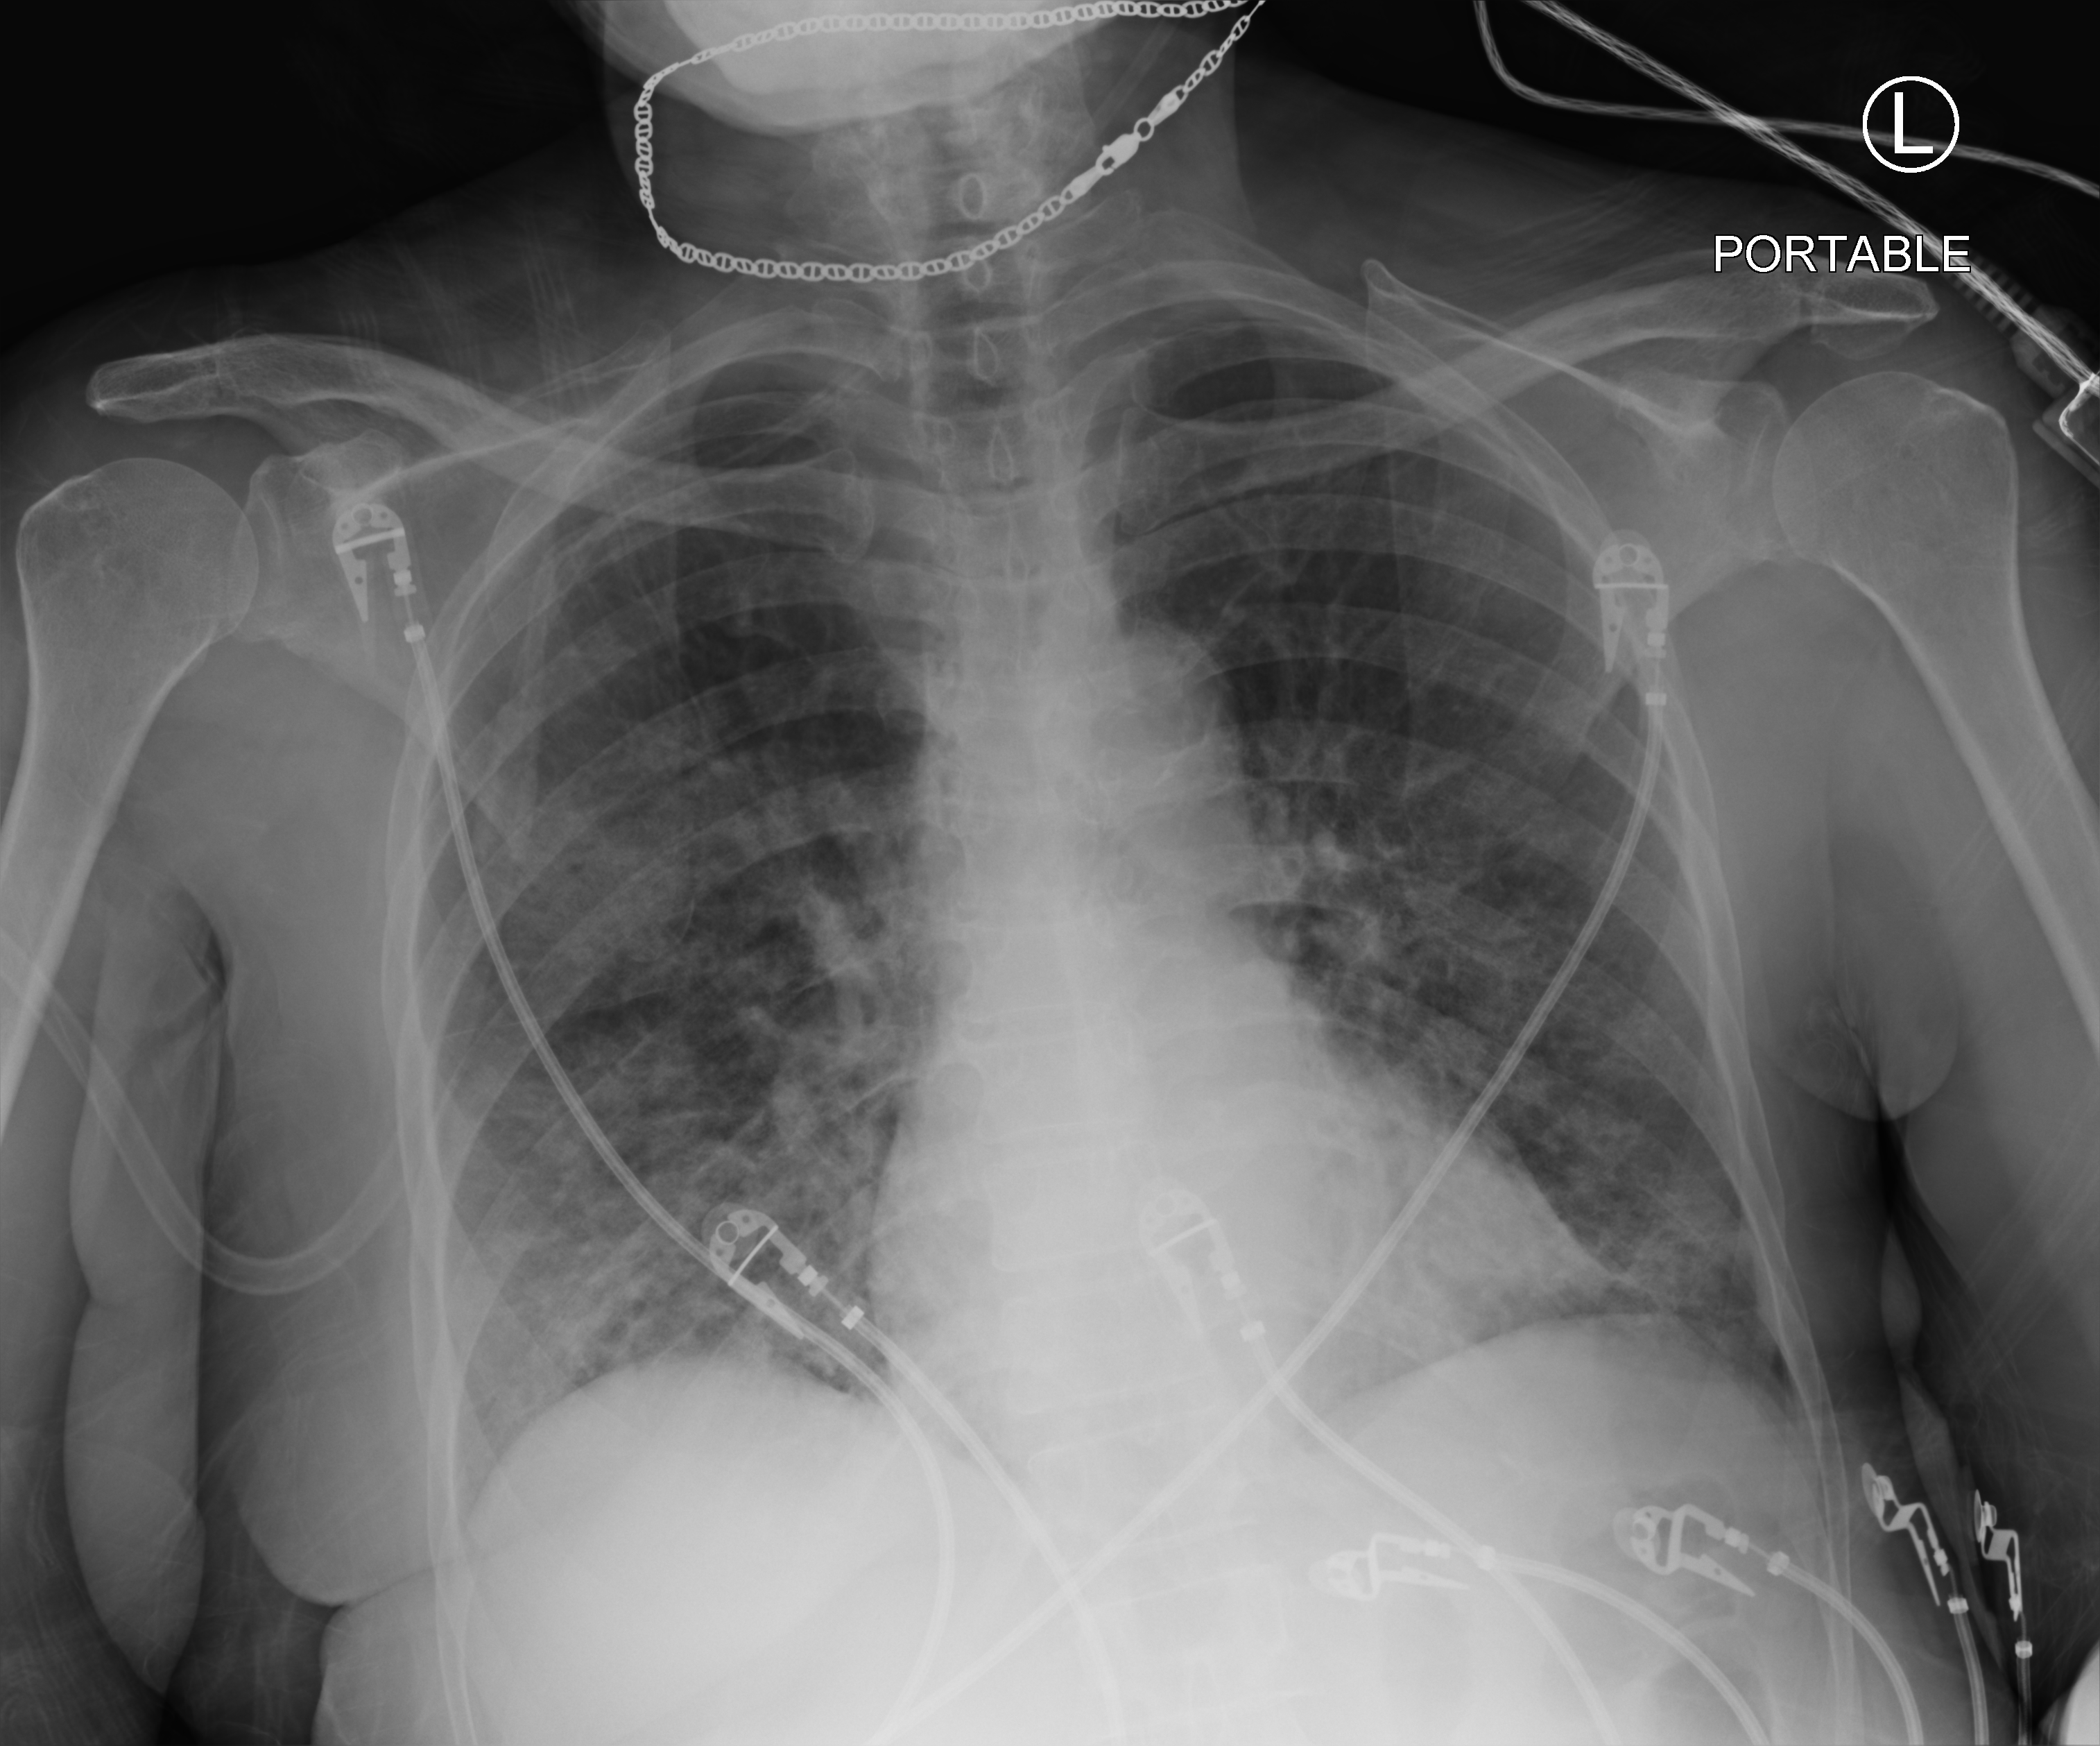
Chest X-ray (portable). Female patient hospitalised with COVID-19, age 75–90 years.
Hospital-stay facts (about this admission, not read from this image; timing relative to this image not recorded): length of hospital stay: 14 days; hypertension (admission record): yes; mechanically ventilated during this hospital stay: no.